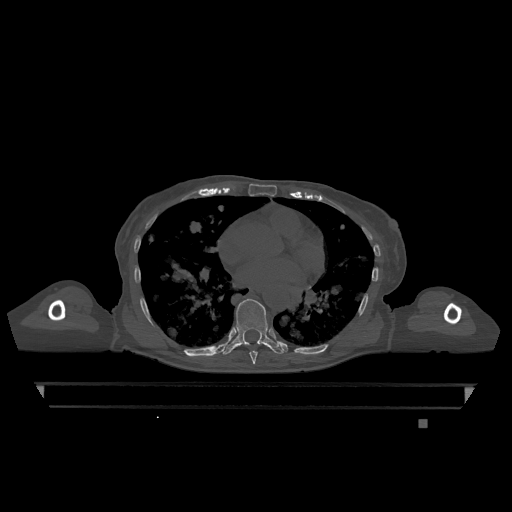
CT including the spine, one axial slice; position 706 of 1317 along the scan axis; bone window (W 1800 / L 400 HU); 0.5 mm slice thickness; 512 × 512 image matrix, field of view 500 × 500 mm. Female patient, age 74 years. From the clinical record (not read from this slice): primary cancer: lung; vertebrae with lytic lesions (as recorded): T1, T4, T5, T6, L4, L5.
Outlined on this slice (semi-automatic segmentation, software-assisted and operator-edited):
- T7 vertebra: bounding box [x1, y1, x2, y2] px = [249, 351, 258, 364]
- T9 vertebra: [222, 299, 284, 355]